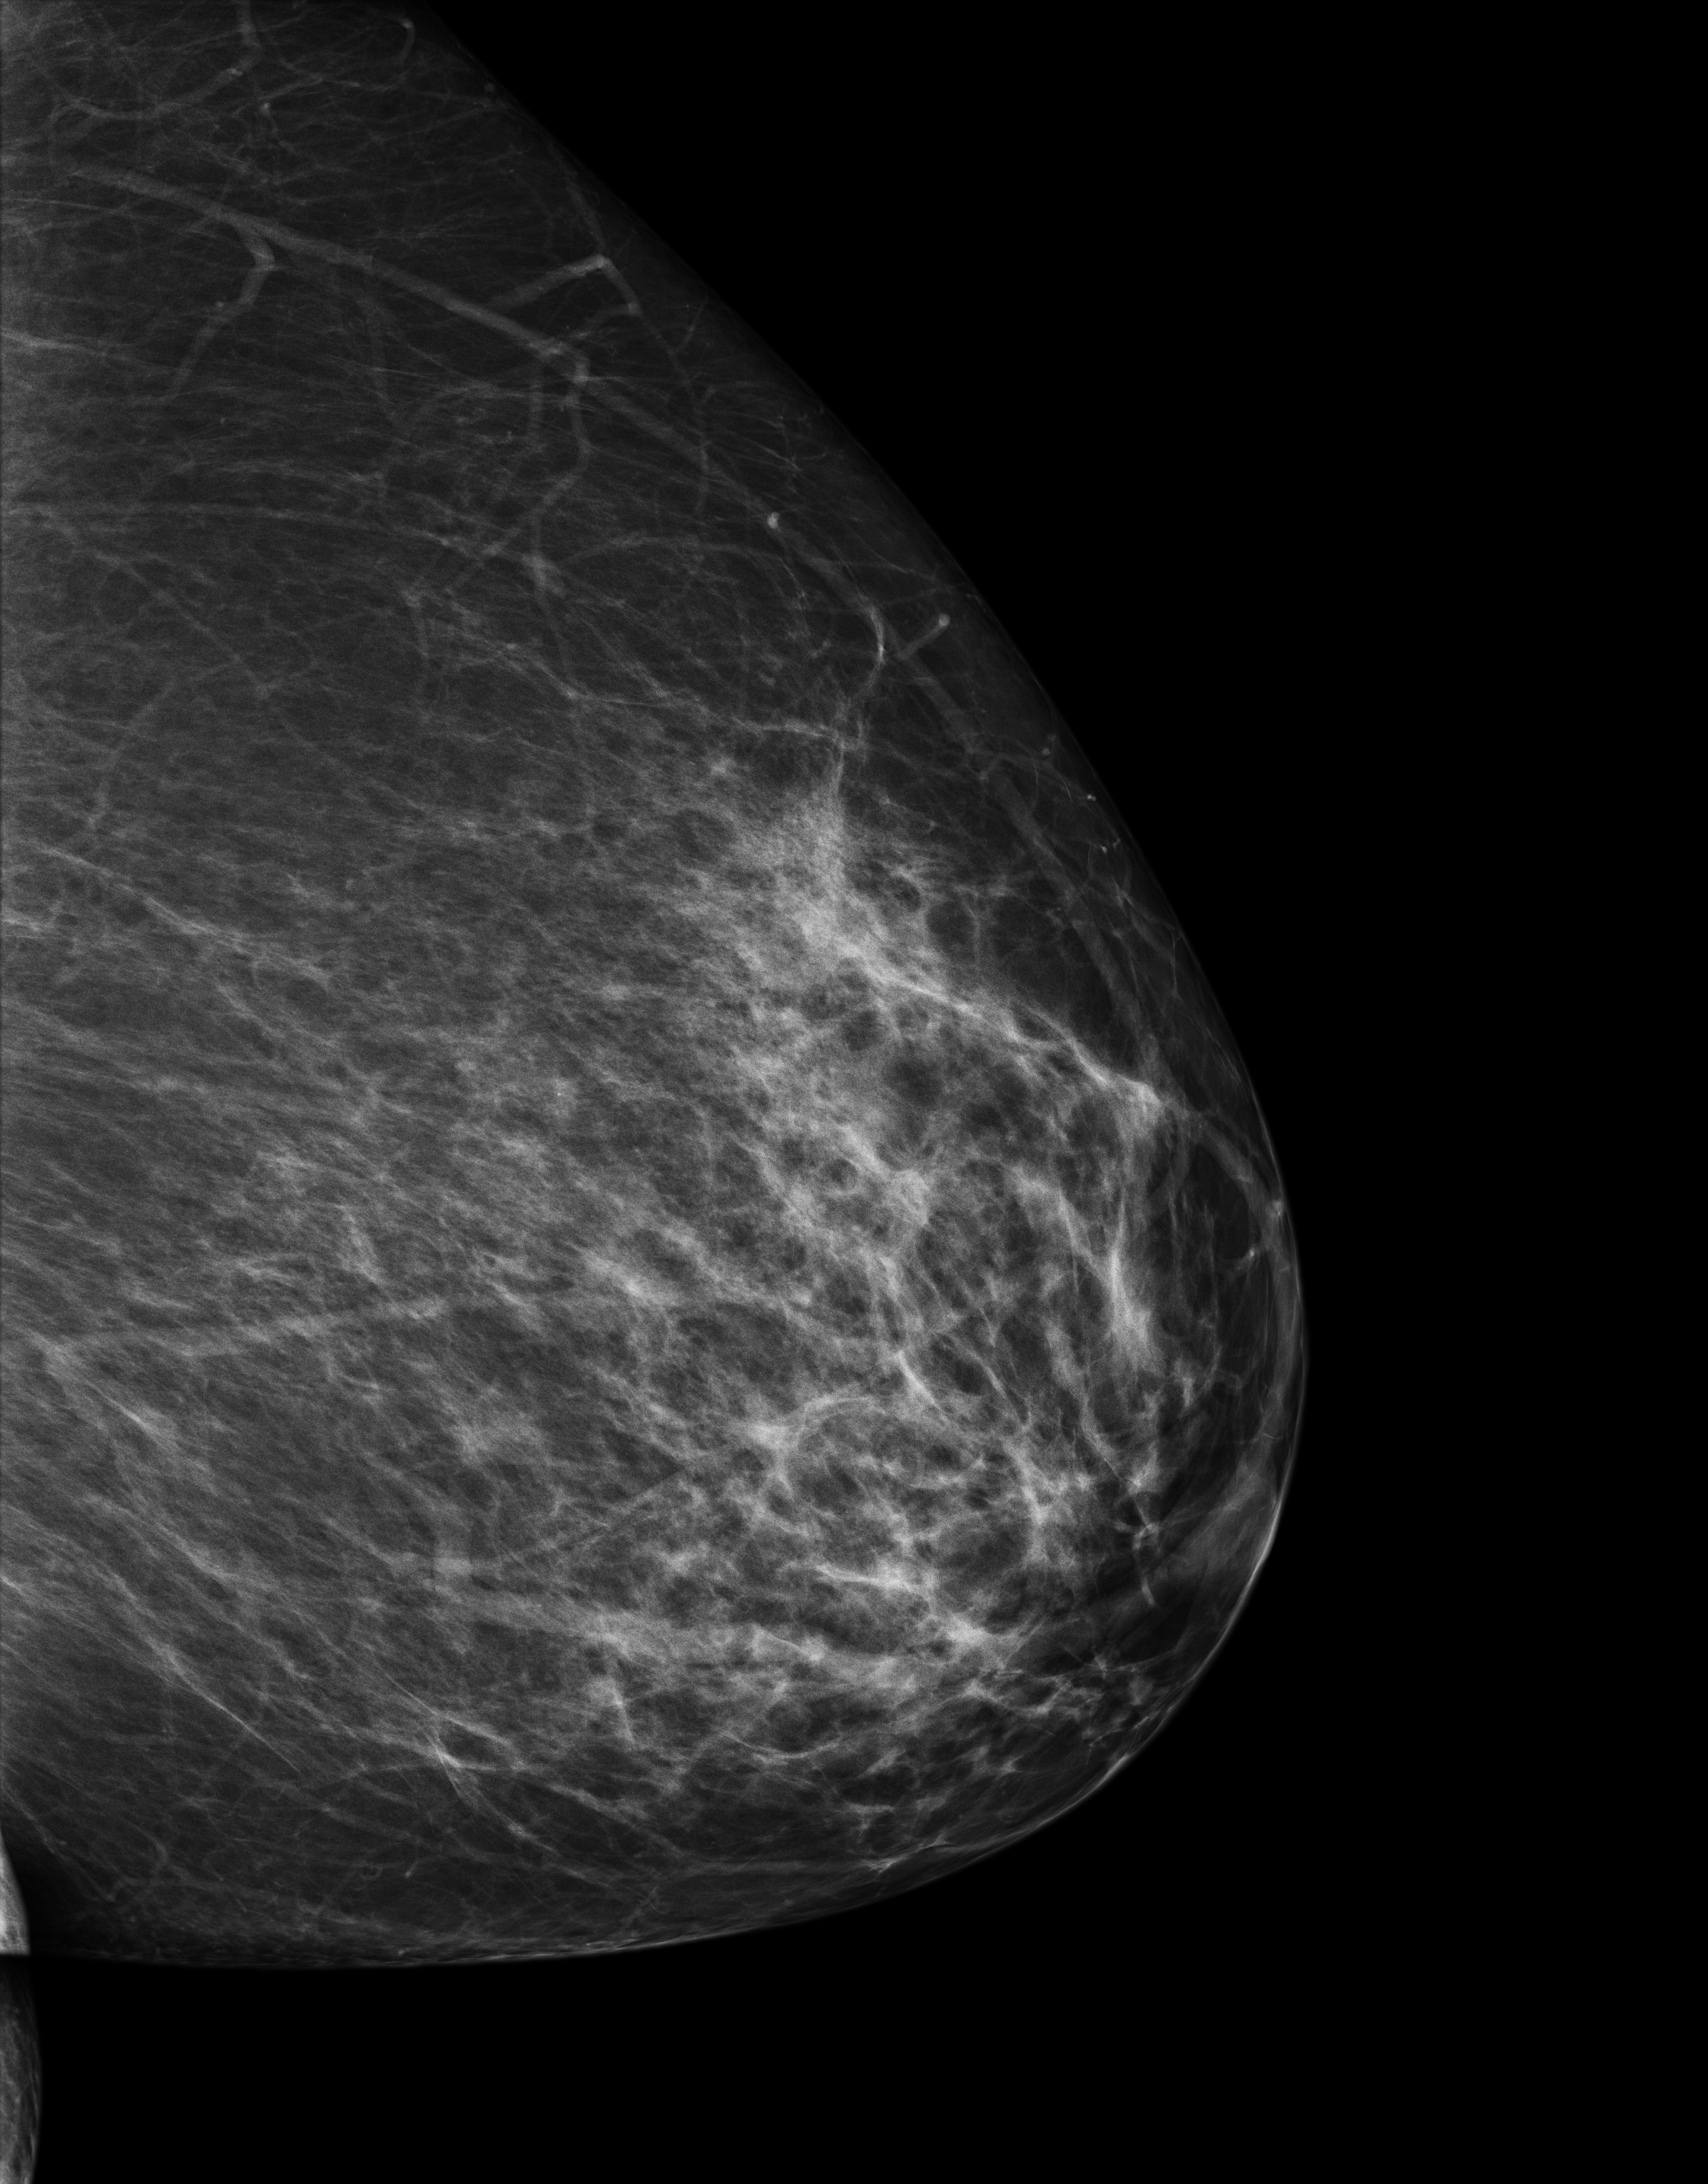
Screening examination. Patient: female, 58 years.
Image type: full-field digital mammogram. Breast: left. Projection: MLO view.